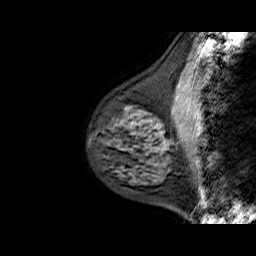
Breast MRI (dynamic contrast-enhanced), one sagittal slice. Position 20 of 60 along the scan axis. Dynamic contrast-enhanced series, time point 2 of 6 at this slice position (early post-contrast). 1.5 T. TE 6.4 ms, TR 32.9 ms. 4 mm slice thickness. 256 × 256 image matrix, field of view 200 × 200 mm. Female patient. From the clinical record (not read from this slice): setting: breast cancer imaged before/during neoadjuvant chemotherapy; receptor status: HR-positive, HER2-negative.
Outlined on this slice (semi-automatic segmentation, software-assisted and operator-edited):
- analysis volume of interest (the breast-tissue region the enhancement analysis was run in; not a lesion): bounding box [x1, y1, x2, y2] px = [93, 94, 168, 175]
- tumour enhancement mask (voxels above the 100 % enhancement threshold inside the analysis volume of interest): [159, 131, 161, 133]